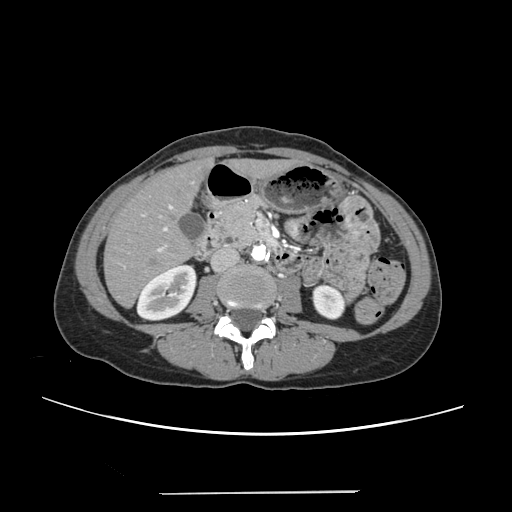
Contrast-enhanced abdominal CT, one axial slice; slice 88 of 240 in the series (ordered by position); 120 kVp; intravenous contrast given; soft-tissue window (W 400 / L 40 HU); 1.25 mm slice thickness; 512 × 512 image matrix, field of view 371 × 371 mm. Female patient, age 60 years. From the clinical record (not read from this slice): diagnosis: colorectal cancer liver metastases, imaged before liver resection; multiple liver metastases: no; largest metastasis: 1.5 cm; chemotherapy before resection: yes.
Annotated regions visible in this slice (expert manual segmentation):
- liver: bounding box <105,162,284,305> (left, top, right, bottom; pixels)
- planned liver remnant (the part of the liver to remain after resection): <105,163,283,305>
- portal vein (with intrahepatic branches): <124,205,172,268>